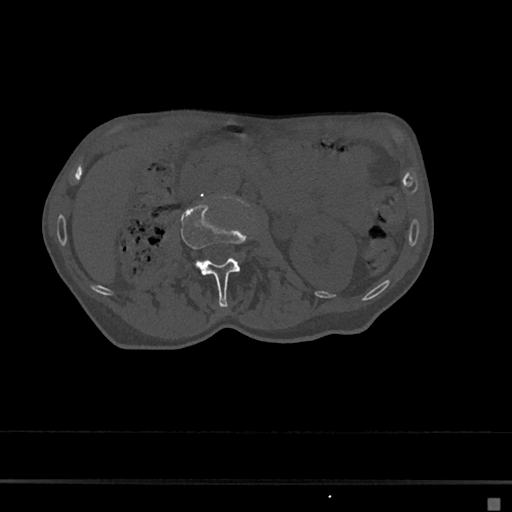
CT including the spine, one axial slice; slice 5 of 797 in the series (ordered by position); reconstruction kernel Br40s/3; 120 kVp; bone window (W 1800 / L 400 HU); 0.5 mm slice thickness; 512 × 512 image matrix. Female patient, age 68 years. From the clinical record (not read from this slice): primary cancer: renal.
Annotated regions visible in this slice (semi-automatic segmentation, software-assisted and operator-edited):
- L2 vertebra: bounding box (x1, y1, x2, y2) in pixels: (181, 202, 251, 306)